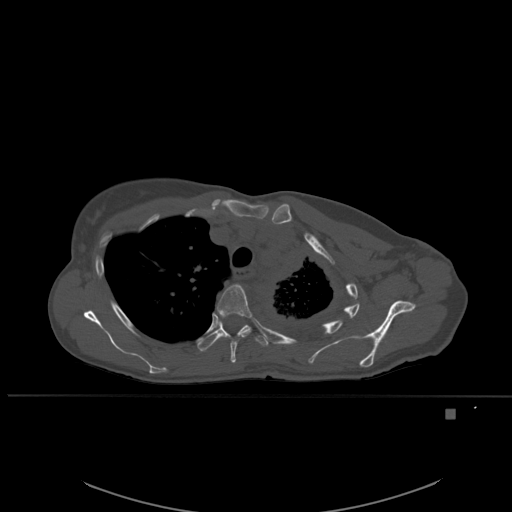
CT including the spine, one axial slice. Position 407 of 537 along the scan axis. Bone window (W 1800 / L 400 HU). 512 × 512 image matrix, field of view 440 × 440 mm. Female patient, age 45 years. From the clinical record (not read from this slice): primary cancer: lung.
Structures marked on this image (semi-automatically segmented with operator editing):
- T4 vertebra: bounding box (x1, y1, x2, y2) in pixels: (217, 284, 252, 363)
- T5 vertebra: (196, 316, 269, 352)